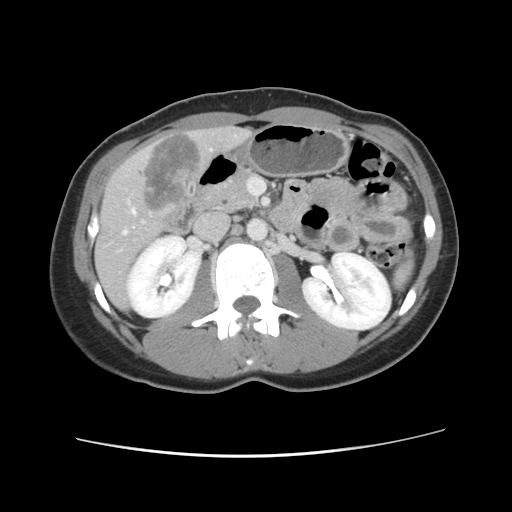
Contrast-enhanced abdominal CT, one axial slice. Slice 42 of 134 in the series (ordered by position). 120 kVp. Soft-tissue window (W 400 / L 40 HU). 2.5 mm slice thickness. 512 × 512 image matrix, field of view 339 × 339 mm. Female patient, age 33 years. From the clinical record (not read from this slice): diagnosis: colorectal cancer liver metastases, imaged before liver resection; multiple liver metastases: yes; largest metastasis: 4.5 cm; chemotherapy before resection: no.
Structures marked on this image (outlined manually by an expert reader):
- hepatic veins: bounding box (x1, y1, x2, y2) in pixels: (123, 208, 136, 235)
- liver: (95, 127, 250, 309)
- planned liver remnant (the part of the liver to remain after resection): (95, 240, 132, 309)
- liver metastasis: (138, 133, 204, 211)